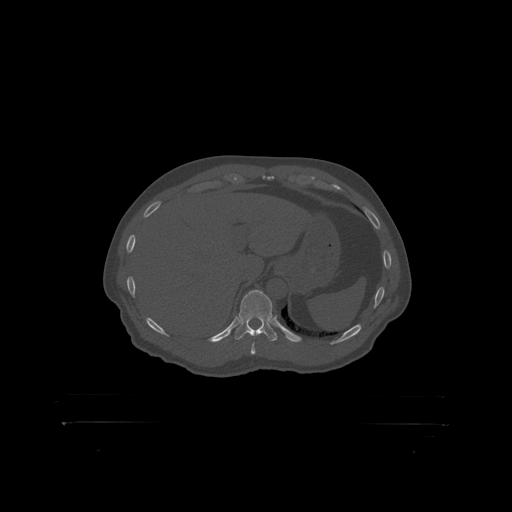
CT including the spine, one axial slice; position 382 of 399 along the scan axis; reconstruction kernel STANDARD; bone window (W 1800 / L 400 HU); 512 × 512 image matrix, field of view 650 × 650 mm. Patient: male, 46 years. From the clinical record (not read from this slice): primary cancer: skin.
Annotated regions visible in this slice (semi-automatic segmentation, software-assisted and operator-edited):
- T11 vertebra: box from (x=239, y=291) to (x=273, y=319) px